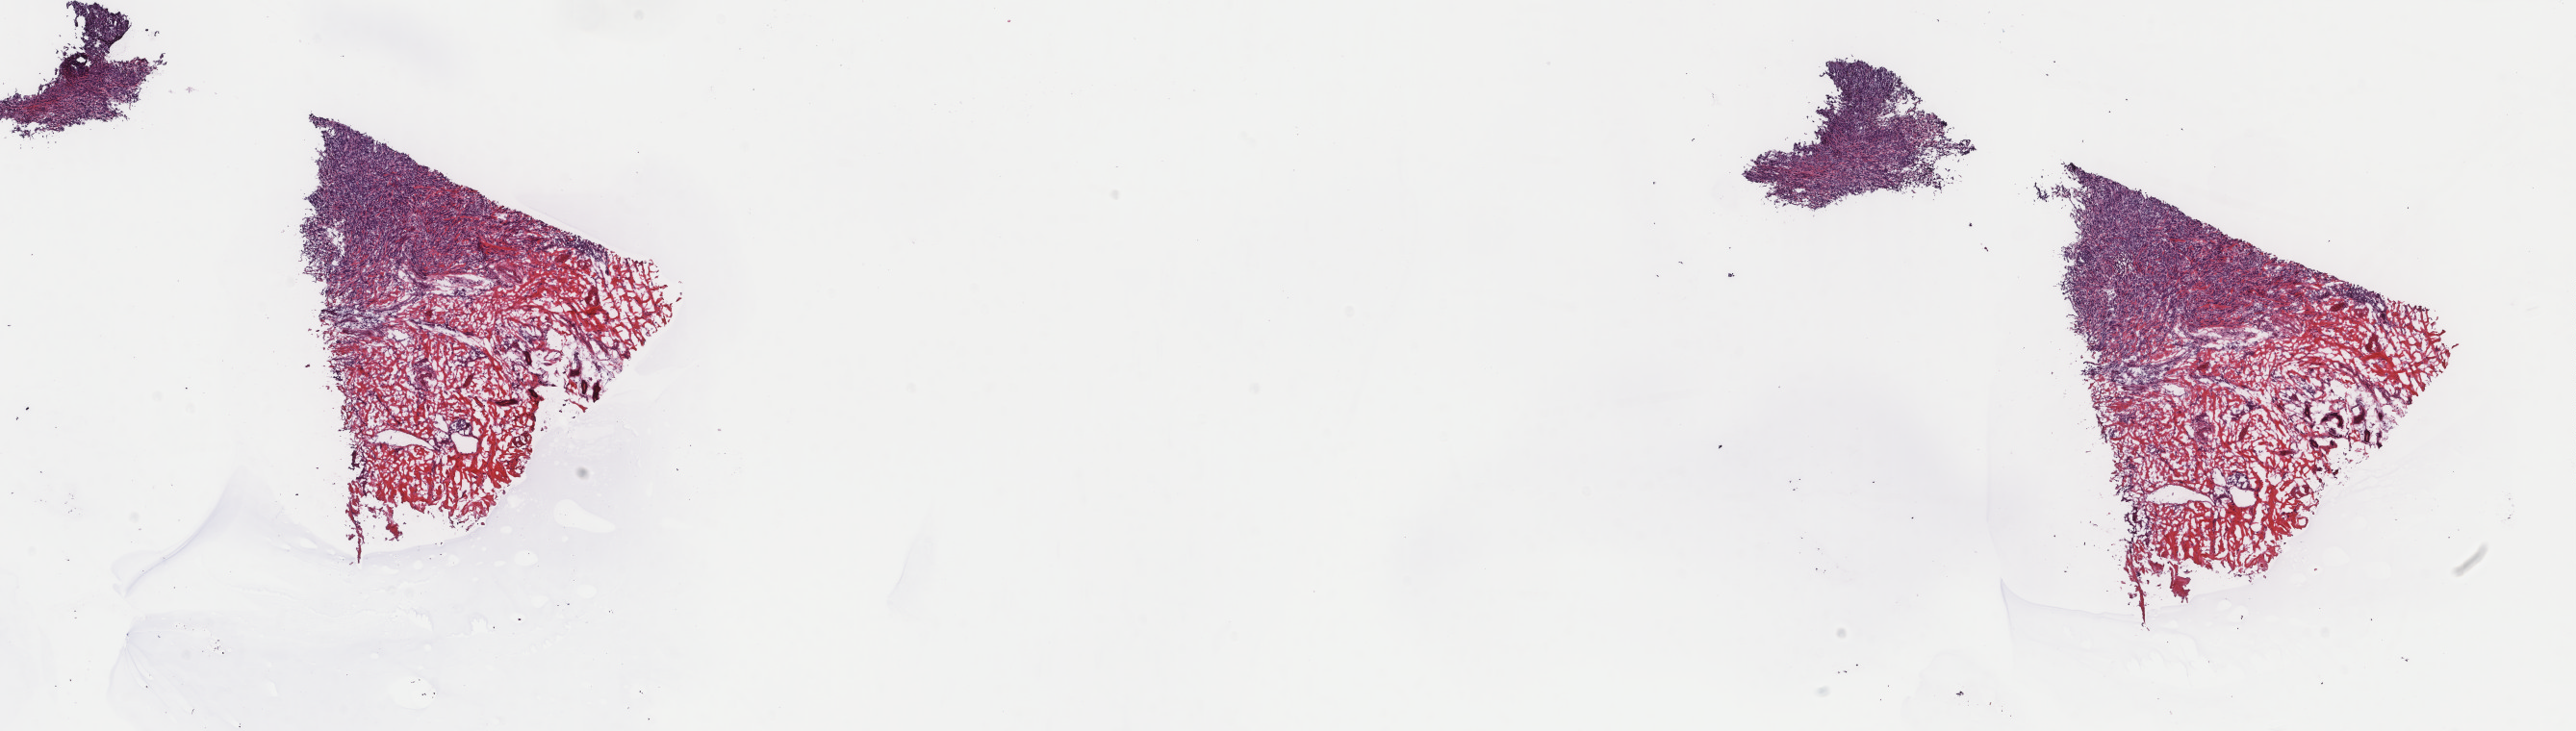
Whole-slide histology image, H&E-stained — low-resolution overview of the scanned area, about 21.2 x 6.0 mm (from a 40x scan); frozen section from the top of the tissue portion; sample: primary tumour, skin. Male, age 63 years at initial diagnosis. Composition of this section per pathologist review: tumour cells 50%, tumour nuclei 75%, normal cells 50%, stromal cells 0%, necrosis 0%. Infiltration values recorded for this section: lymphocyte infiltration 0%, monocyte infiltration 0%, neutrophil infiltration 0%.
* TNM: T4b N0 M0
* AJCC pathologic stage: IIC (7th edition)
* diagnosis: Malignant melanoma, NOS